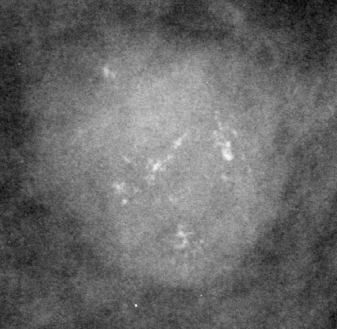
Region of interest cut from a scanned film mammogram (one marked finding); left breast; CC view.
Calcifications, morphology pleomorphic, distribution clustered; BI-RADS assessment category 4; pathology (as recorded): benign.